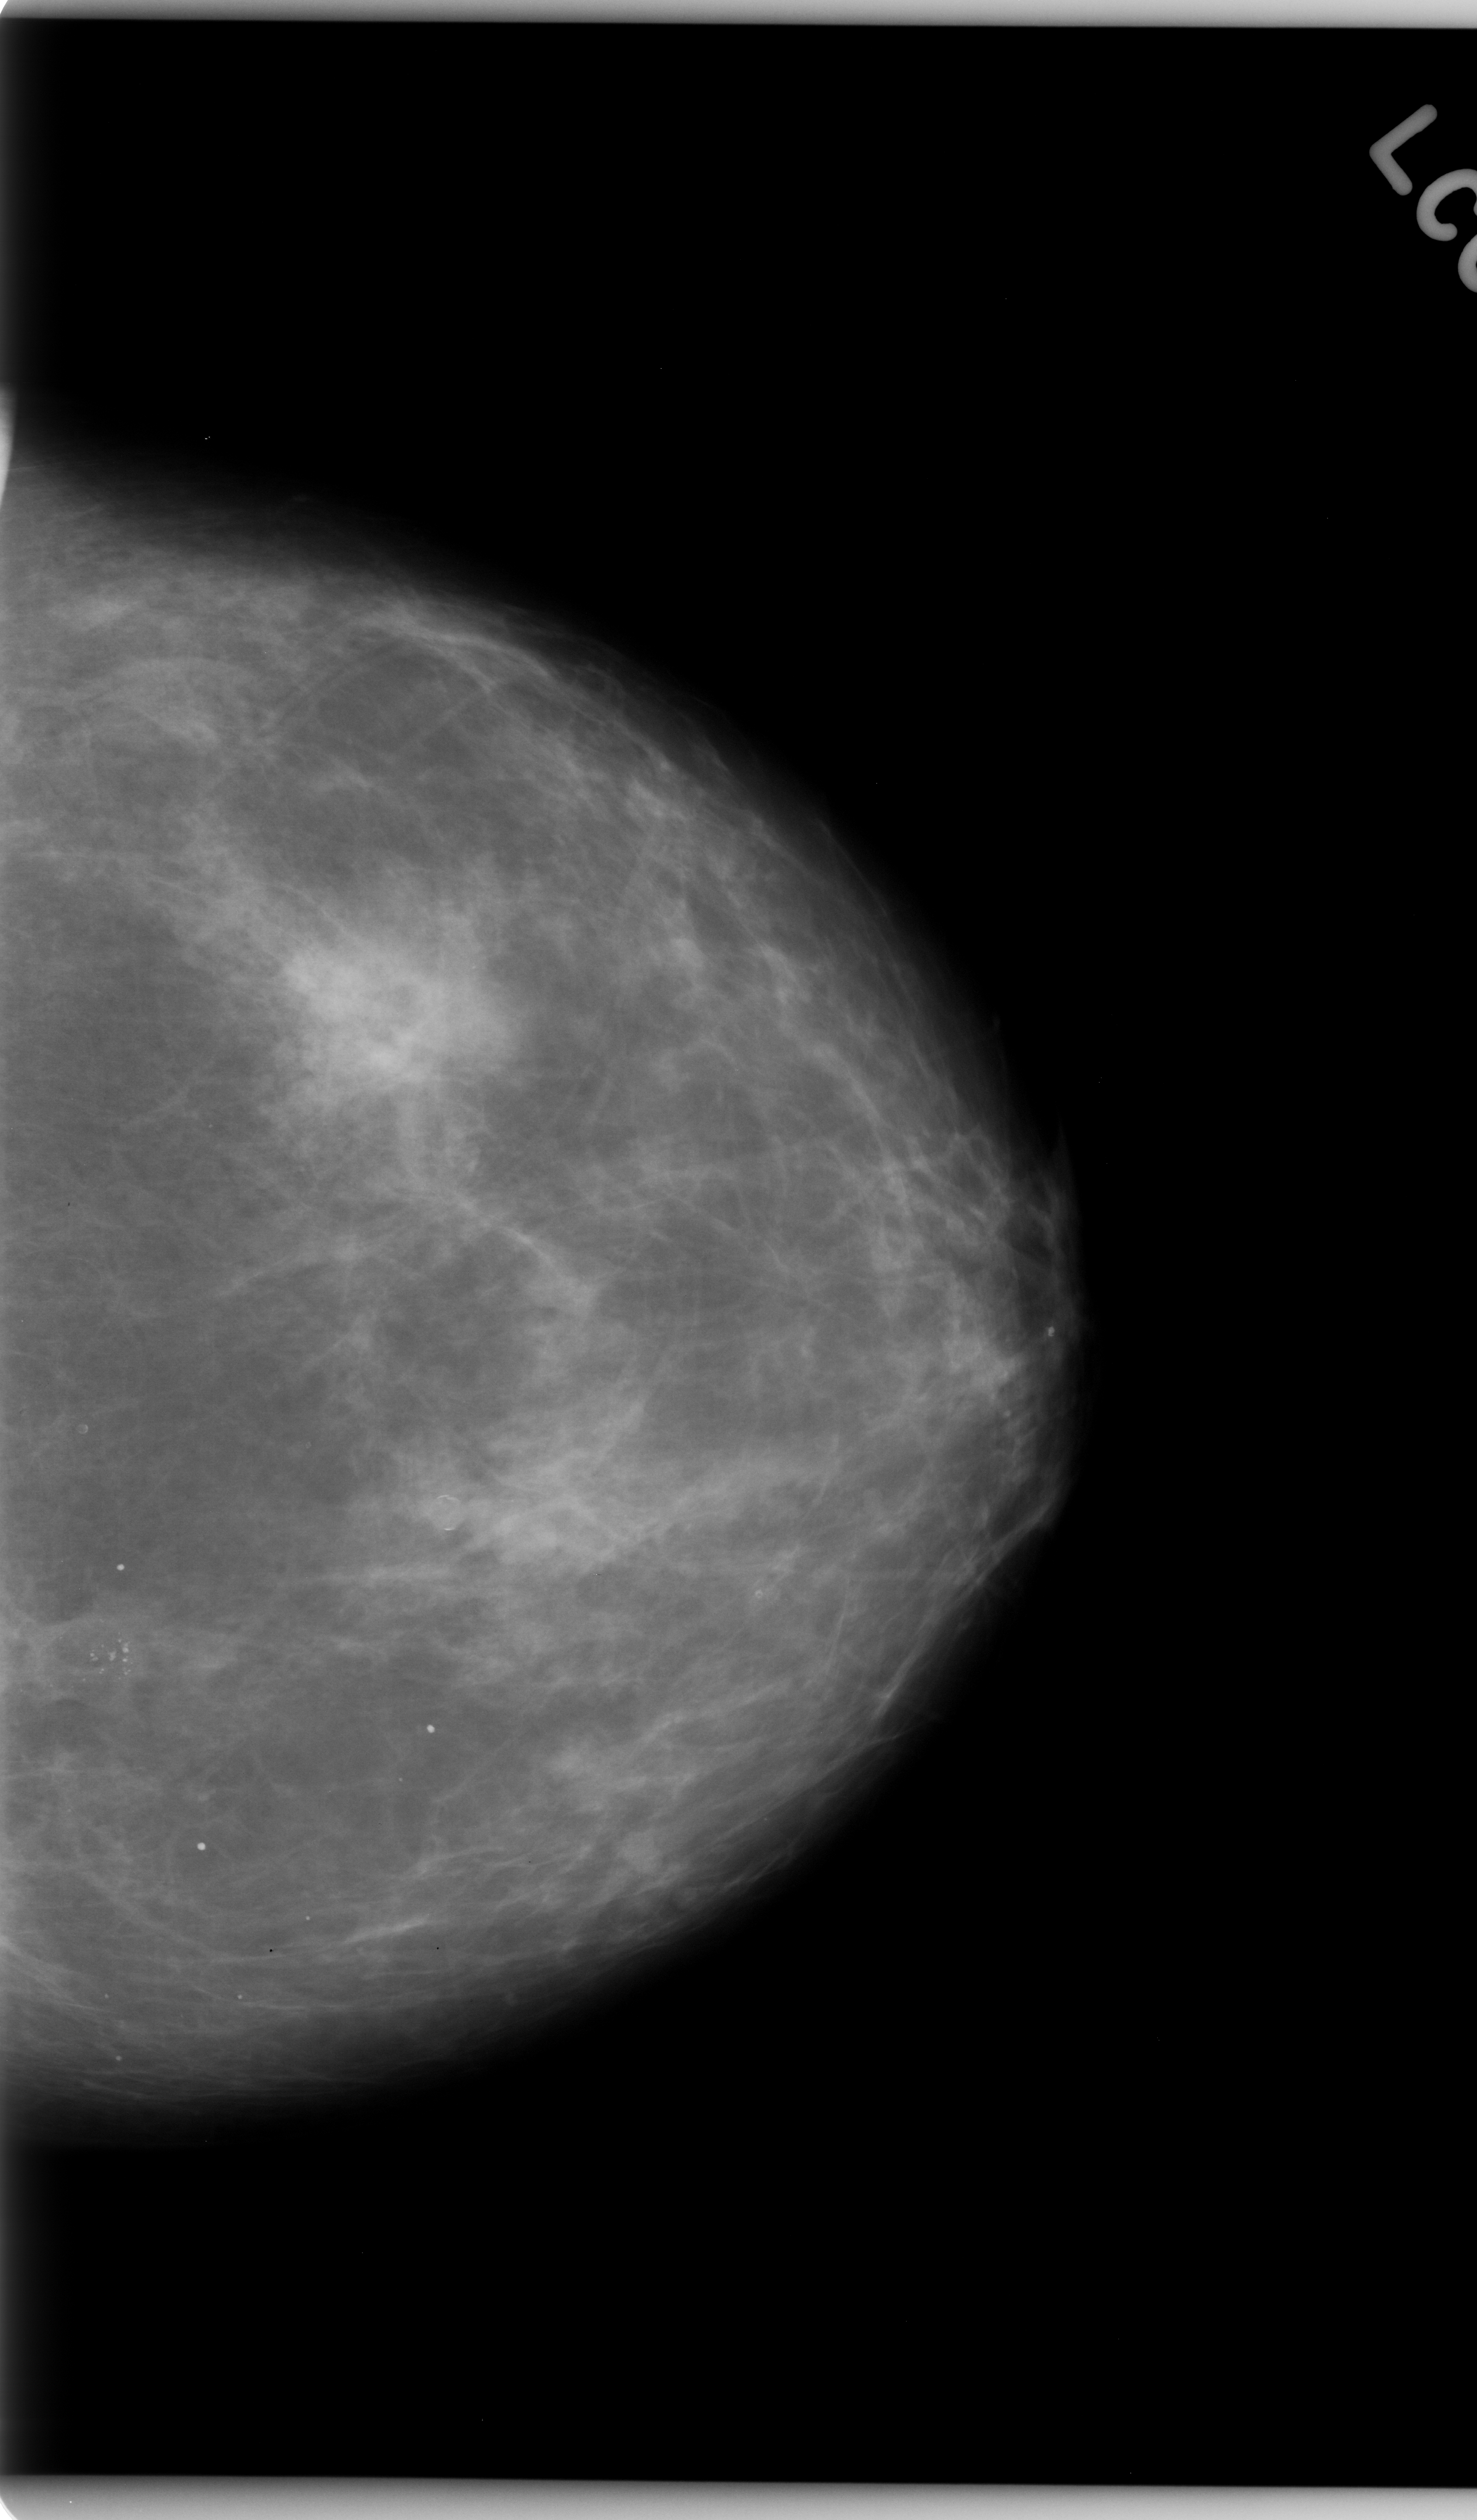
Scanned film-screen mammogram. Left breast. CC view. BI-RADS breast density category 2 (scale 1–4). 1477 × 2520 image matrix.
Expert-marked regions of interest on this film, with their recorded descriptors:
- calcifications, morphology amorphous, distribution clustered; BI-RADS assessment category 4; subtlety rating 5 on a 1 (subtle) to 5 (obvious) scale; pathology (as recorded): benign: bounding box <44,1514,186,1755> (left, top, right, bottom; pixels)